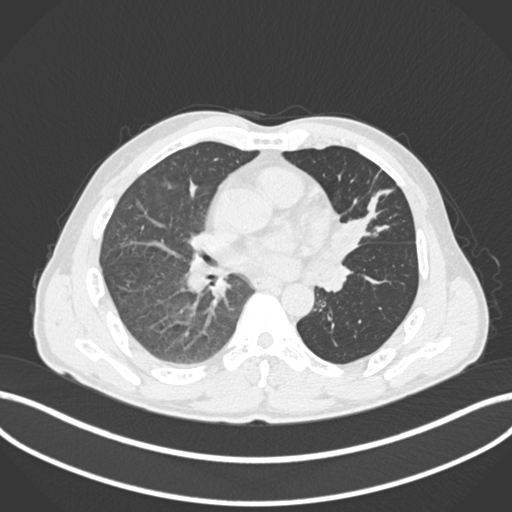
Chest CT, one axial slice; slice 90 of 255 in the series (ordered by position); reconstruction kernel B30f; 120 kVp; lung window (W 1500 / L -600 HU); 1 mm slice thickness; 512 × 512 image matrix, field of view 400 × 400 mm. Male patient, age 57 years. Case-level facts recorded for this patient, not image findings: clinical TNM (as recorded): T2b N0 M0.
Structures marked on this image (bounding box drawn by a radiologist):
- lung tumour (recorded histology: squamous cell carcinoma): bounding box [x1, y1, x2, y2] px = [326, 209, 370, 287]